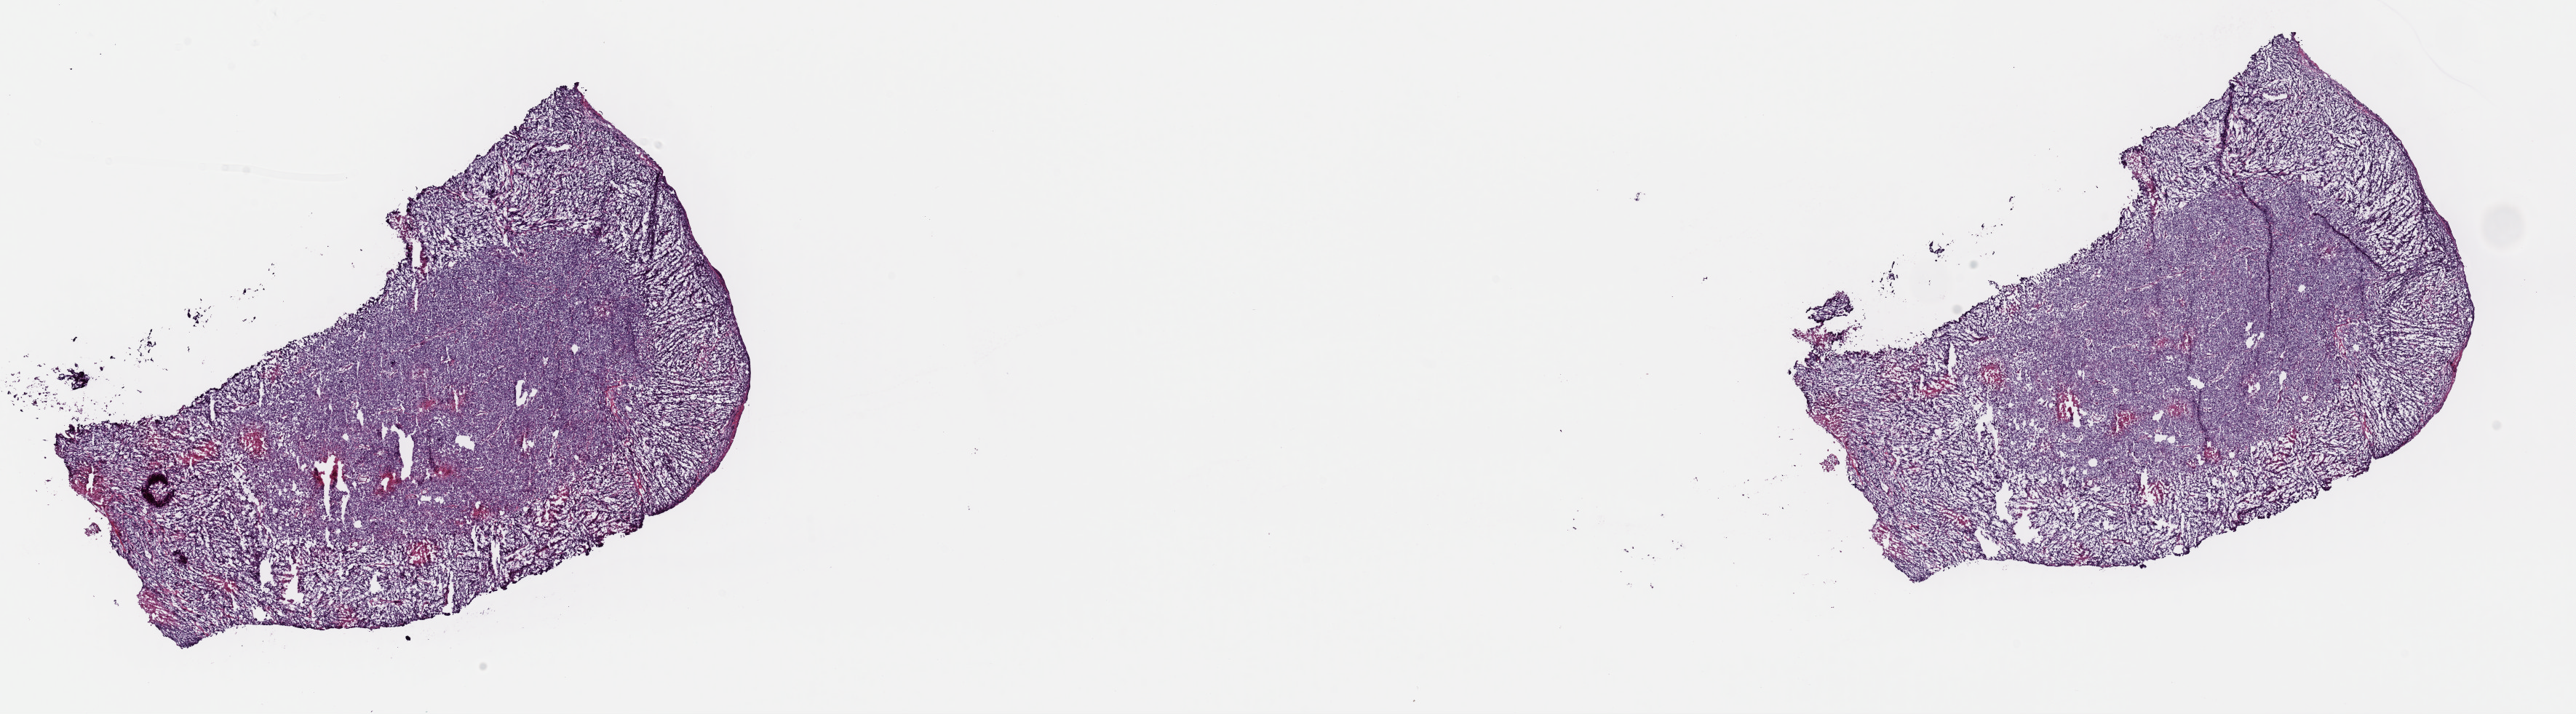
Digitized H&E tissue section (whole slide), whole scanned area (about 28.0 x 7.7 mm, acquisition: 40x scan) shown as a low-resolution overview. Frozen section from the top of the tissue portion. Metastatic tumour sample, sampled site: skin. Male, age 68 years at initial diagnosis. Pathologist review of this section (percent, as recorded): tumour cells 93%, tumour nuclei 92%, normal cells 0%, stromal cells 0%, necrosis 7%. Inflammatory infiltration, as recorded: lymphocyte infiltration 0%, monocyte infiltration 0%, neutrophil infiltration 0%.
This section: metastatic tumour tissue. Patient diagnosis: Malignant melanoma, NOS.